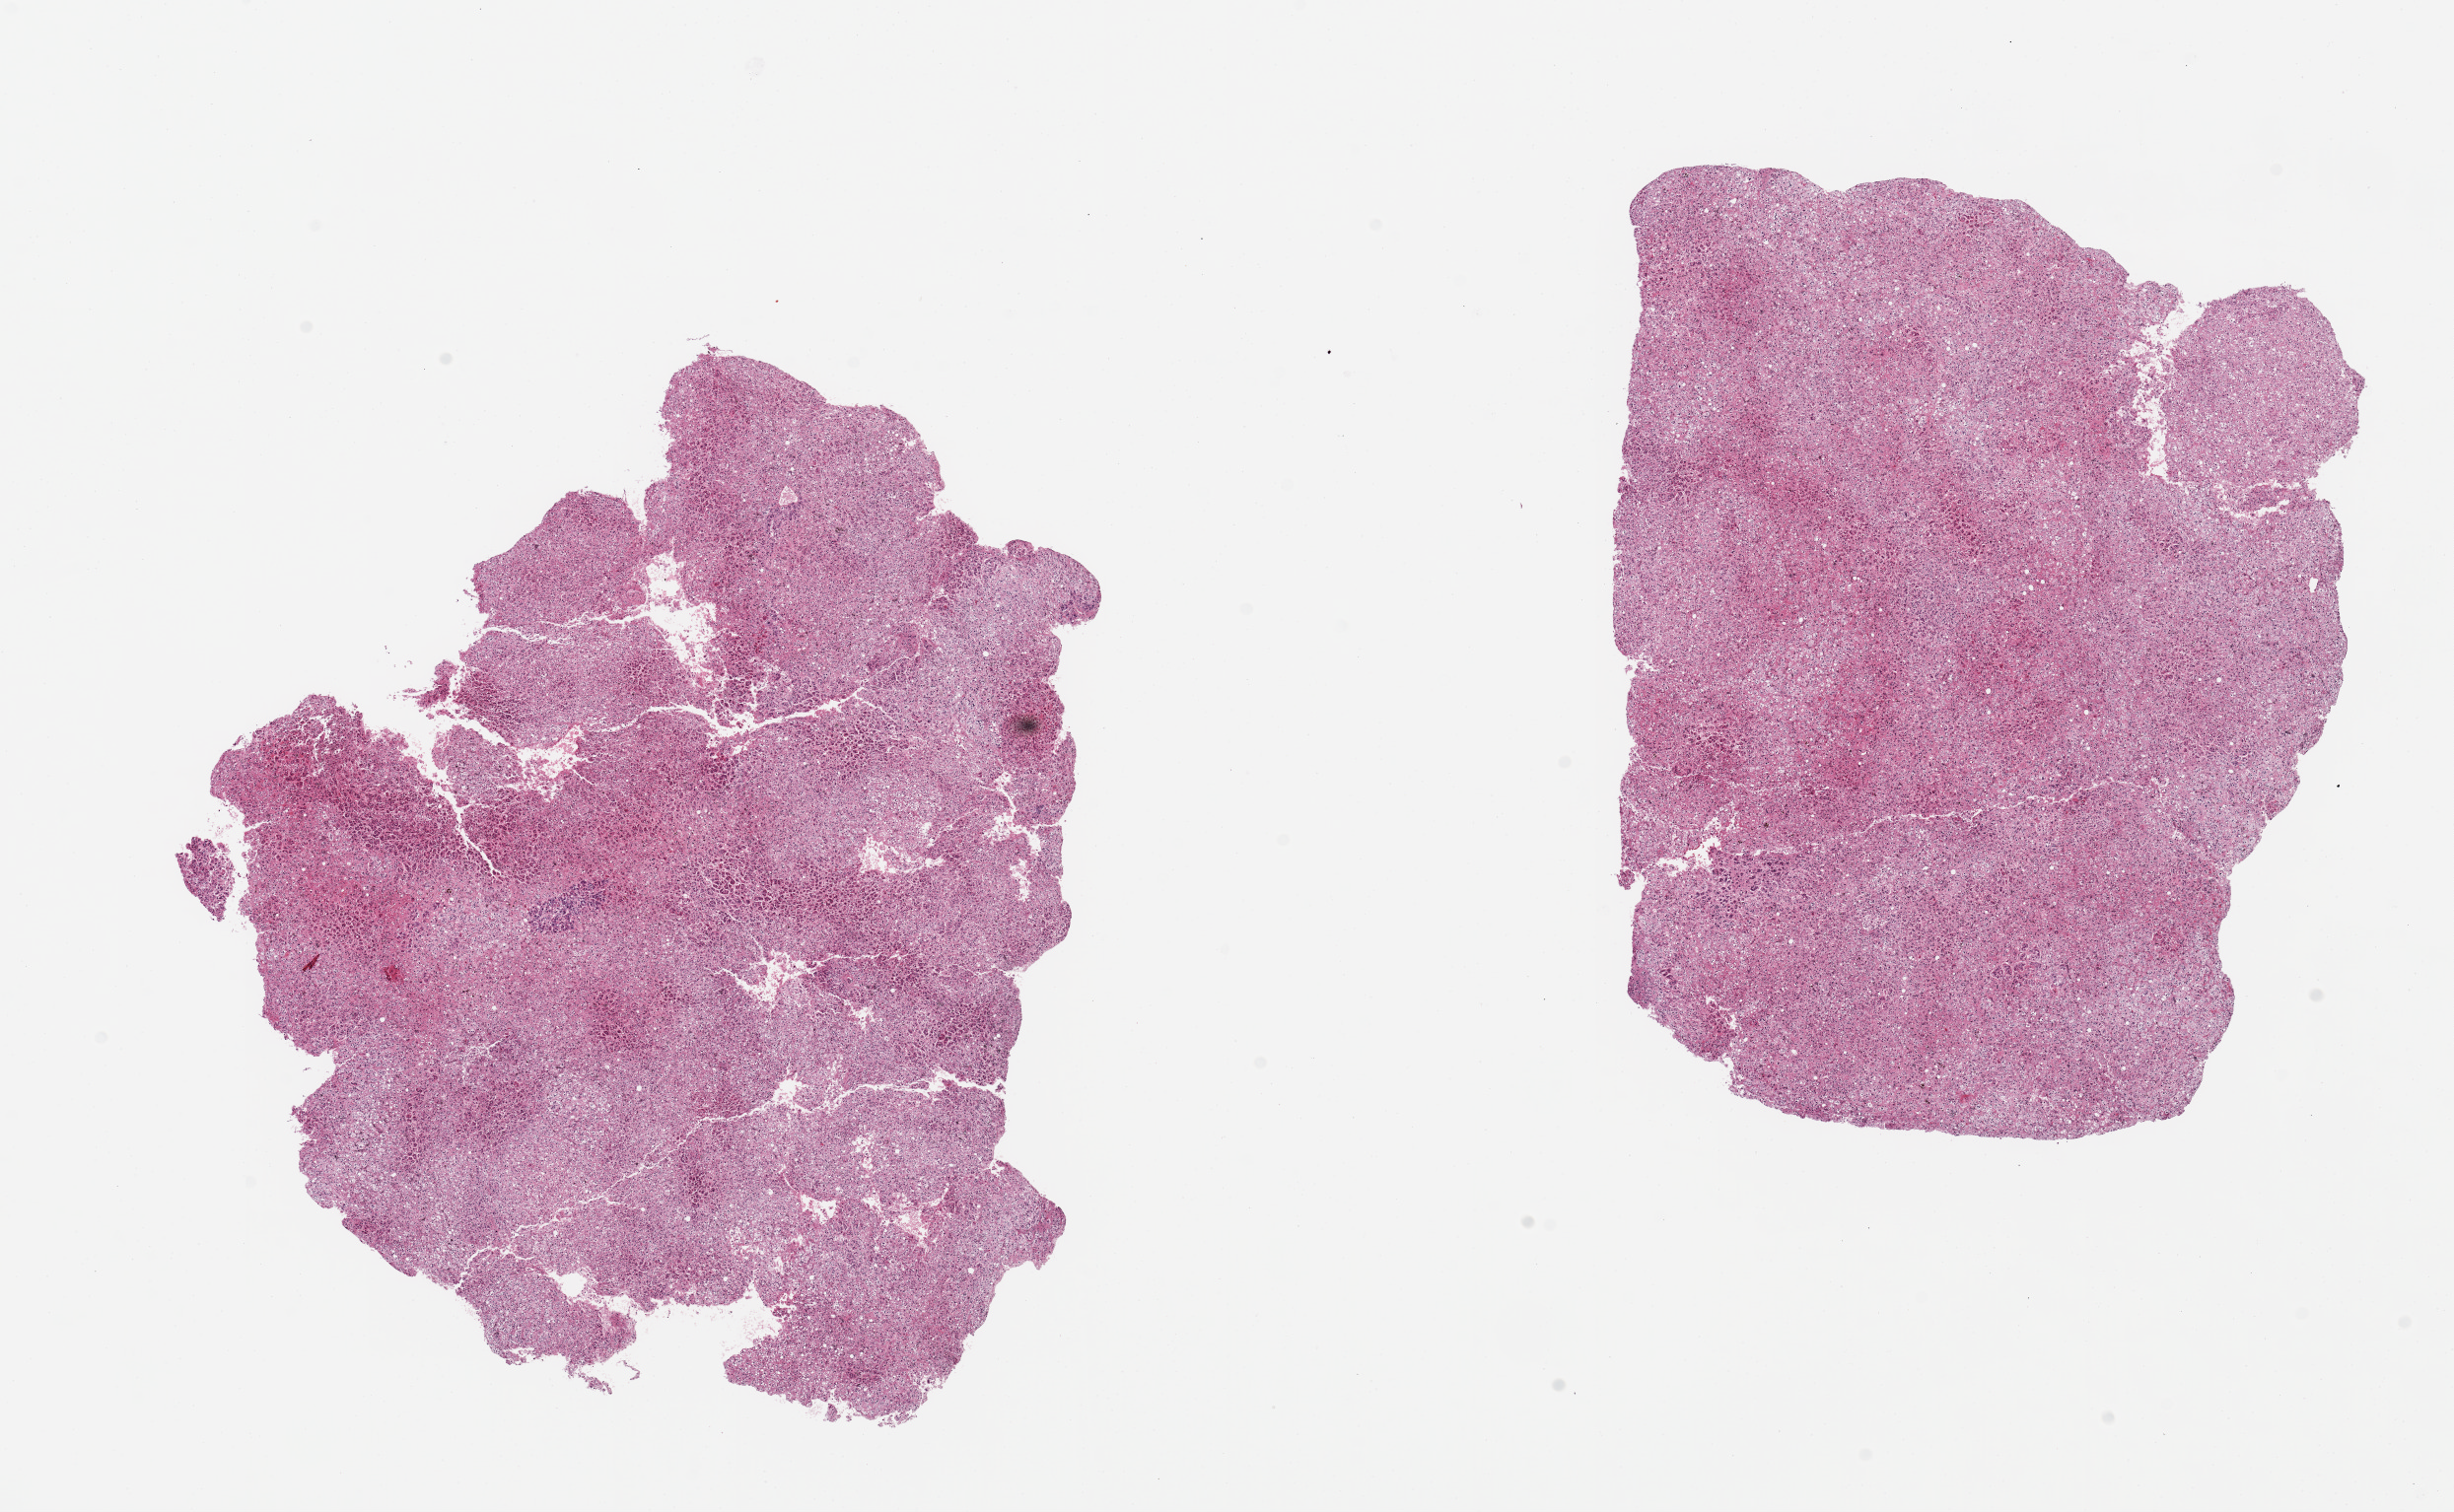
Haematoxylin and eosin whole-slide image, brightfield, whole scanned area (about 19.7 x 12.1 mm, acquisition: 20x scan) shown as a low-resolution overview; PAXgene-fixed, paraffin-embedded tissue; sampled site (target tissue): adrenal gland; donor tissue sample. Donor sex: male.
Pathologist's review note for this sample: 2 pieces 9x7 & 8x6mm; All cortex, badly autolzyed.